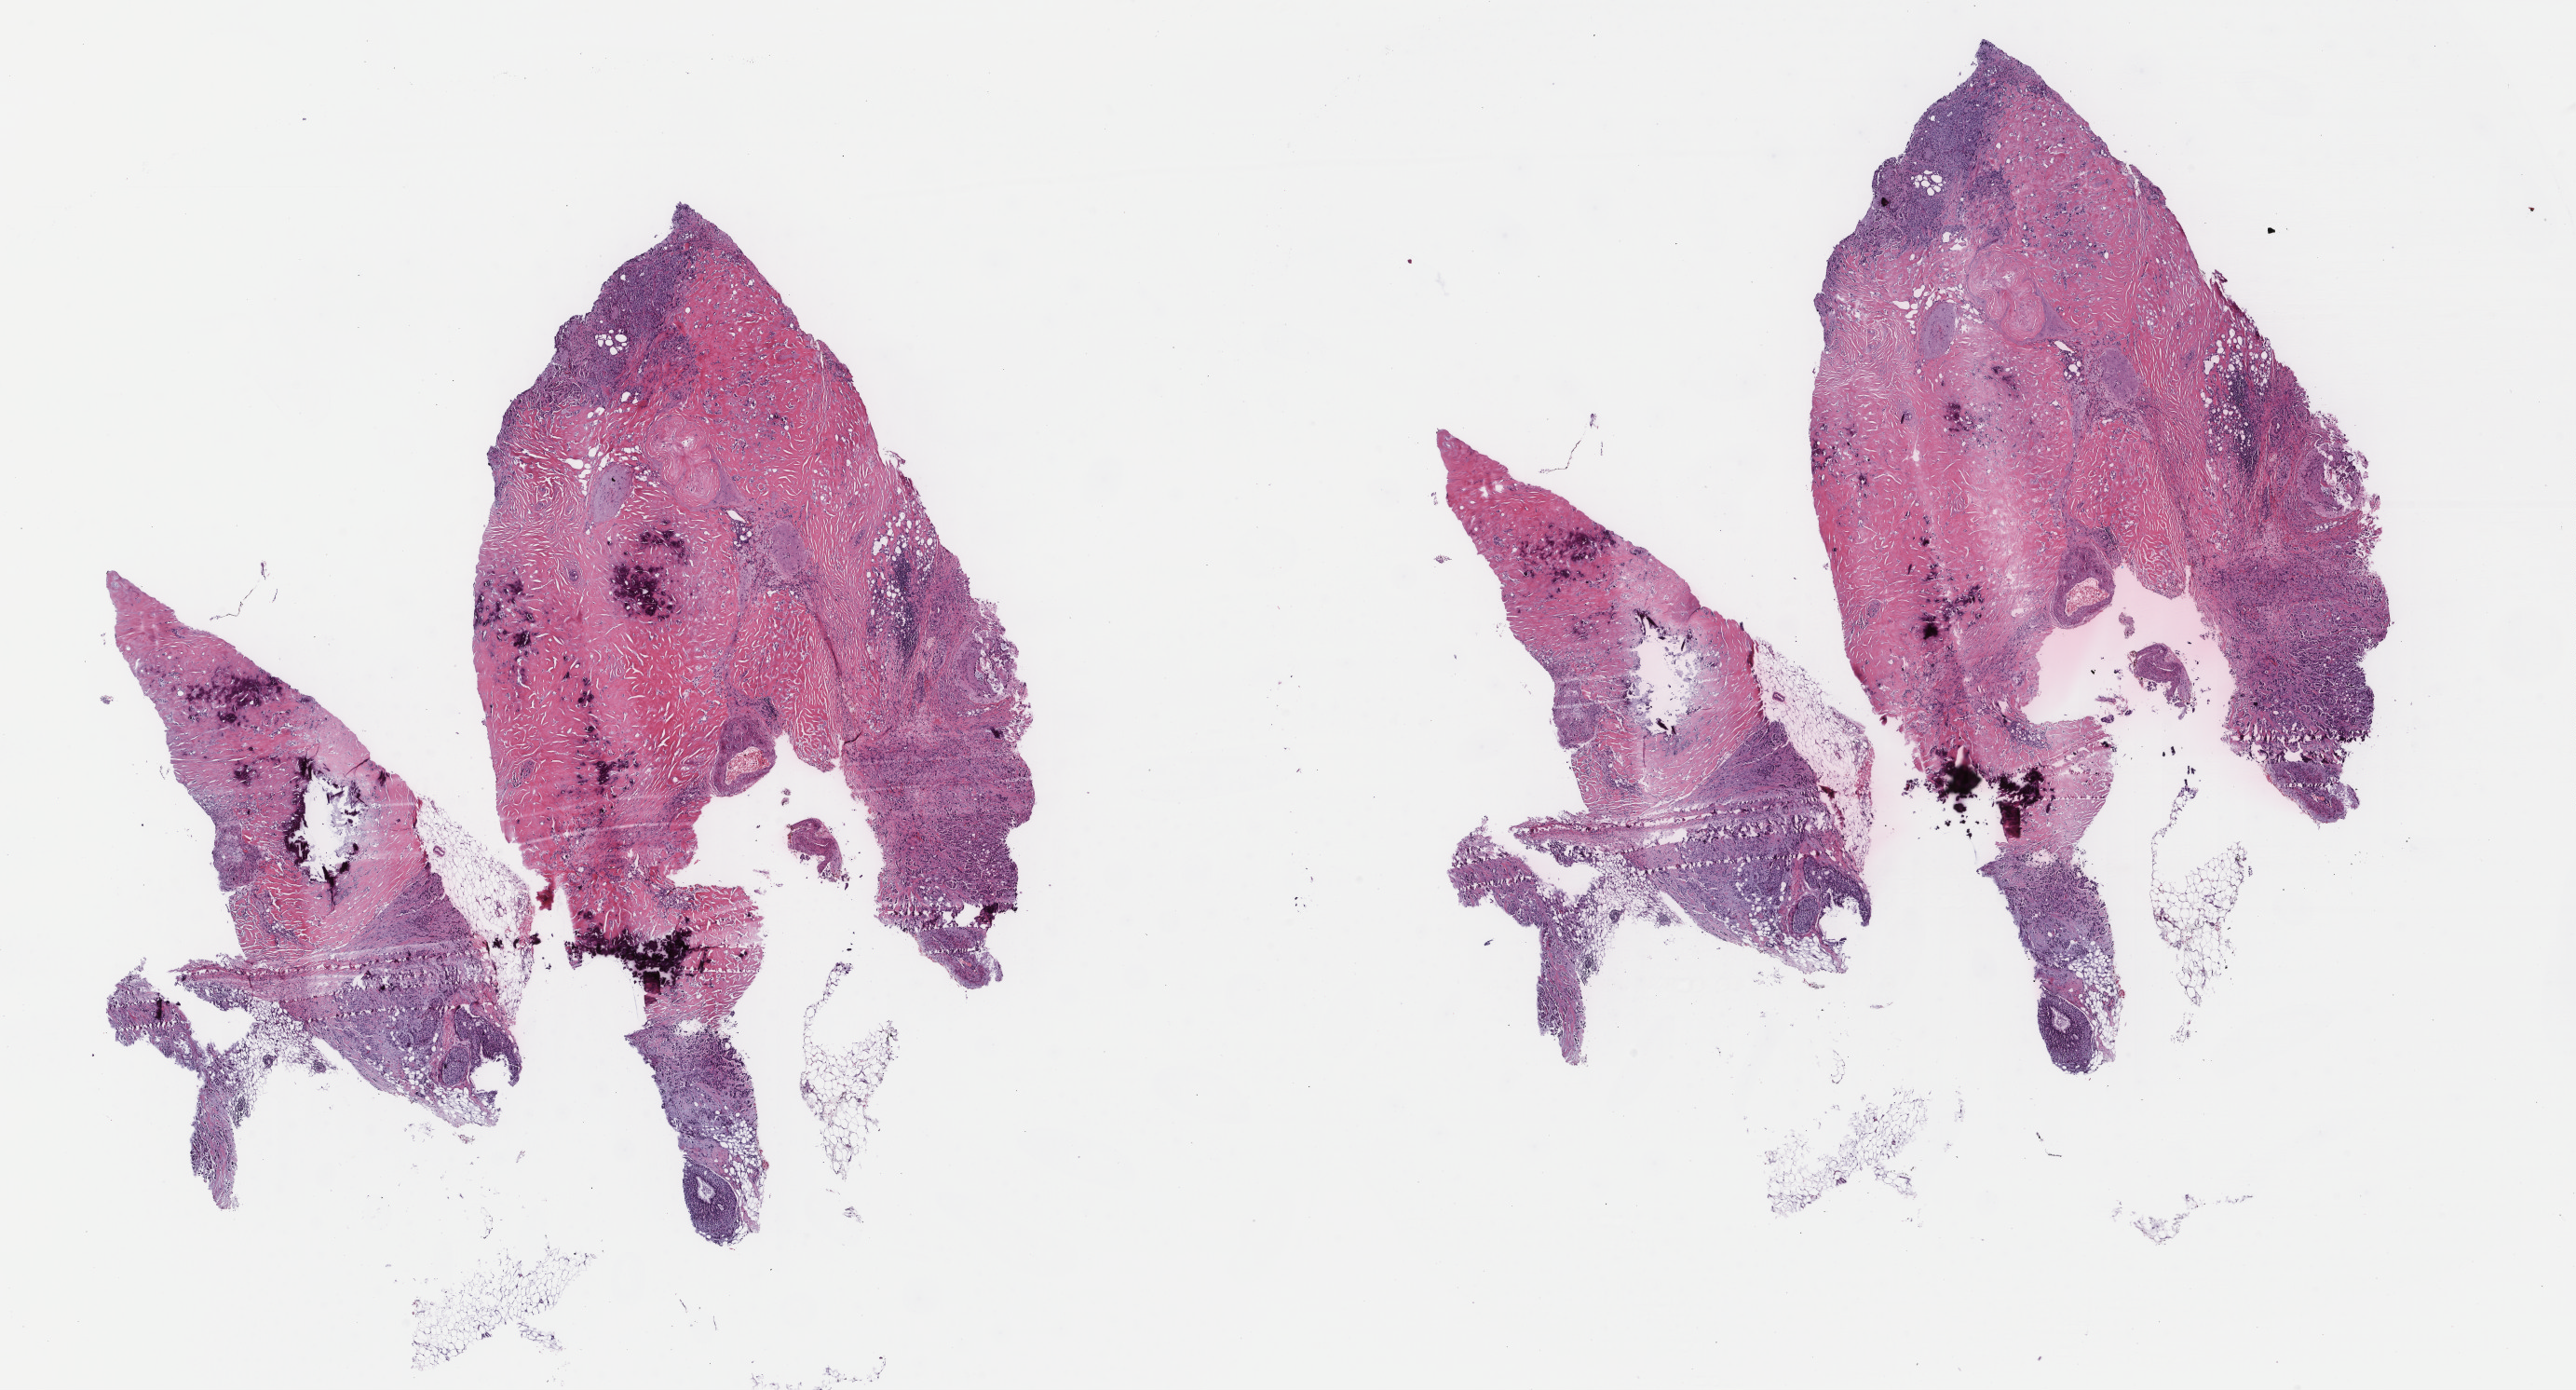
Hematoxylin and eosin (H&E) stained whole-slide image, shown as a low-resolution overview of the whole scanned area (about 22.0 x 11.8 mm, slide scanned at 40x); formalin-fixed paraffin-embedded (FFPE) diagnostic section; breast, primary tumour sample. Female patient; age at initial diagnosis 72 years.
Pathologic diagnosis: Infiltrating duct carcinoma, NOS. TNM: T1 N1a M0. AJCC pathologic stage: IIA. Laterality: left.